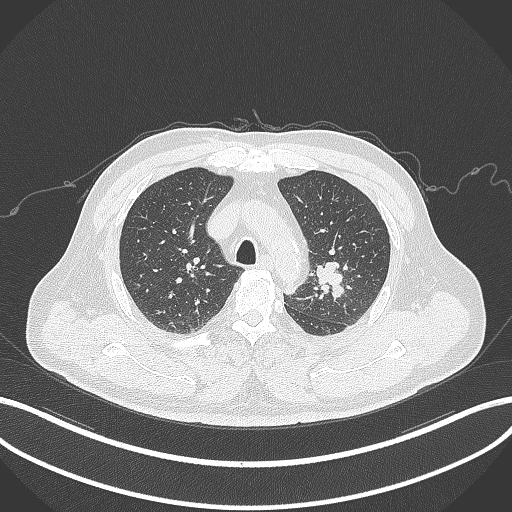
Chest CT, one axial slice. Slice 230 of 286 in the series (ordered by position). 120 kVp. Lung window (W 1500 / L -600 HU). 512 × 512 image matrix, field of view 400 × 400 mm. Male patient, age 67 years. From the clinical record (not read from this slice): clinical TNM (as recorded): T2a N1 M0; histopathological grade: G3.
Outlined on this slice (rectangle marked by the reading radiologist):
- lung tumour (recorded histology: adenocarcinoma): bounding box (x1, y1, x2, y2) in pixels: (313, 257, 349, 304)